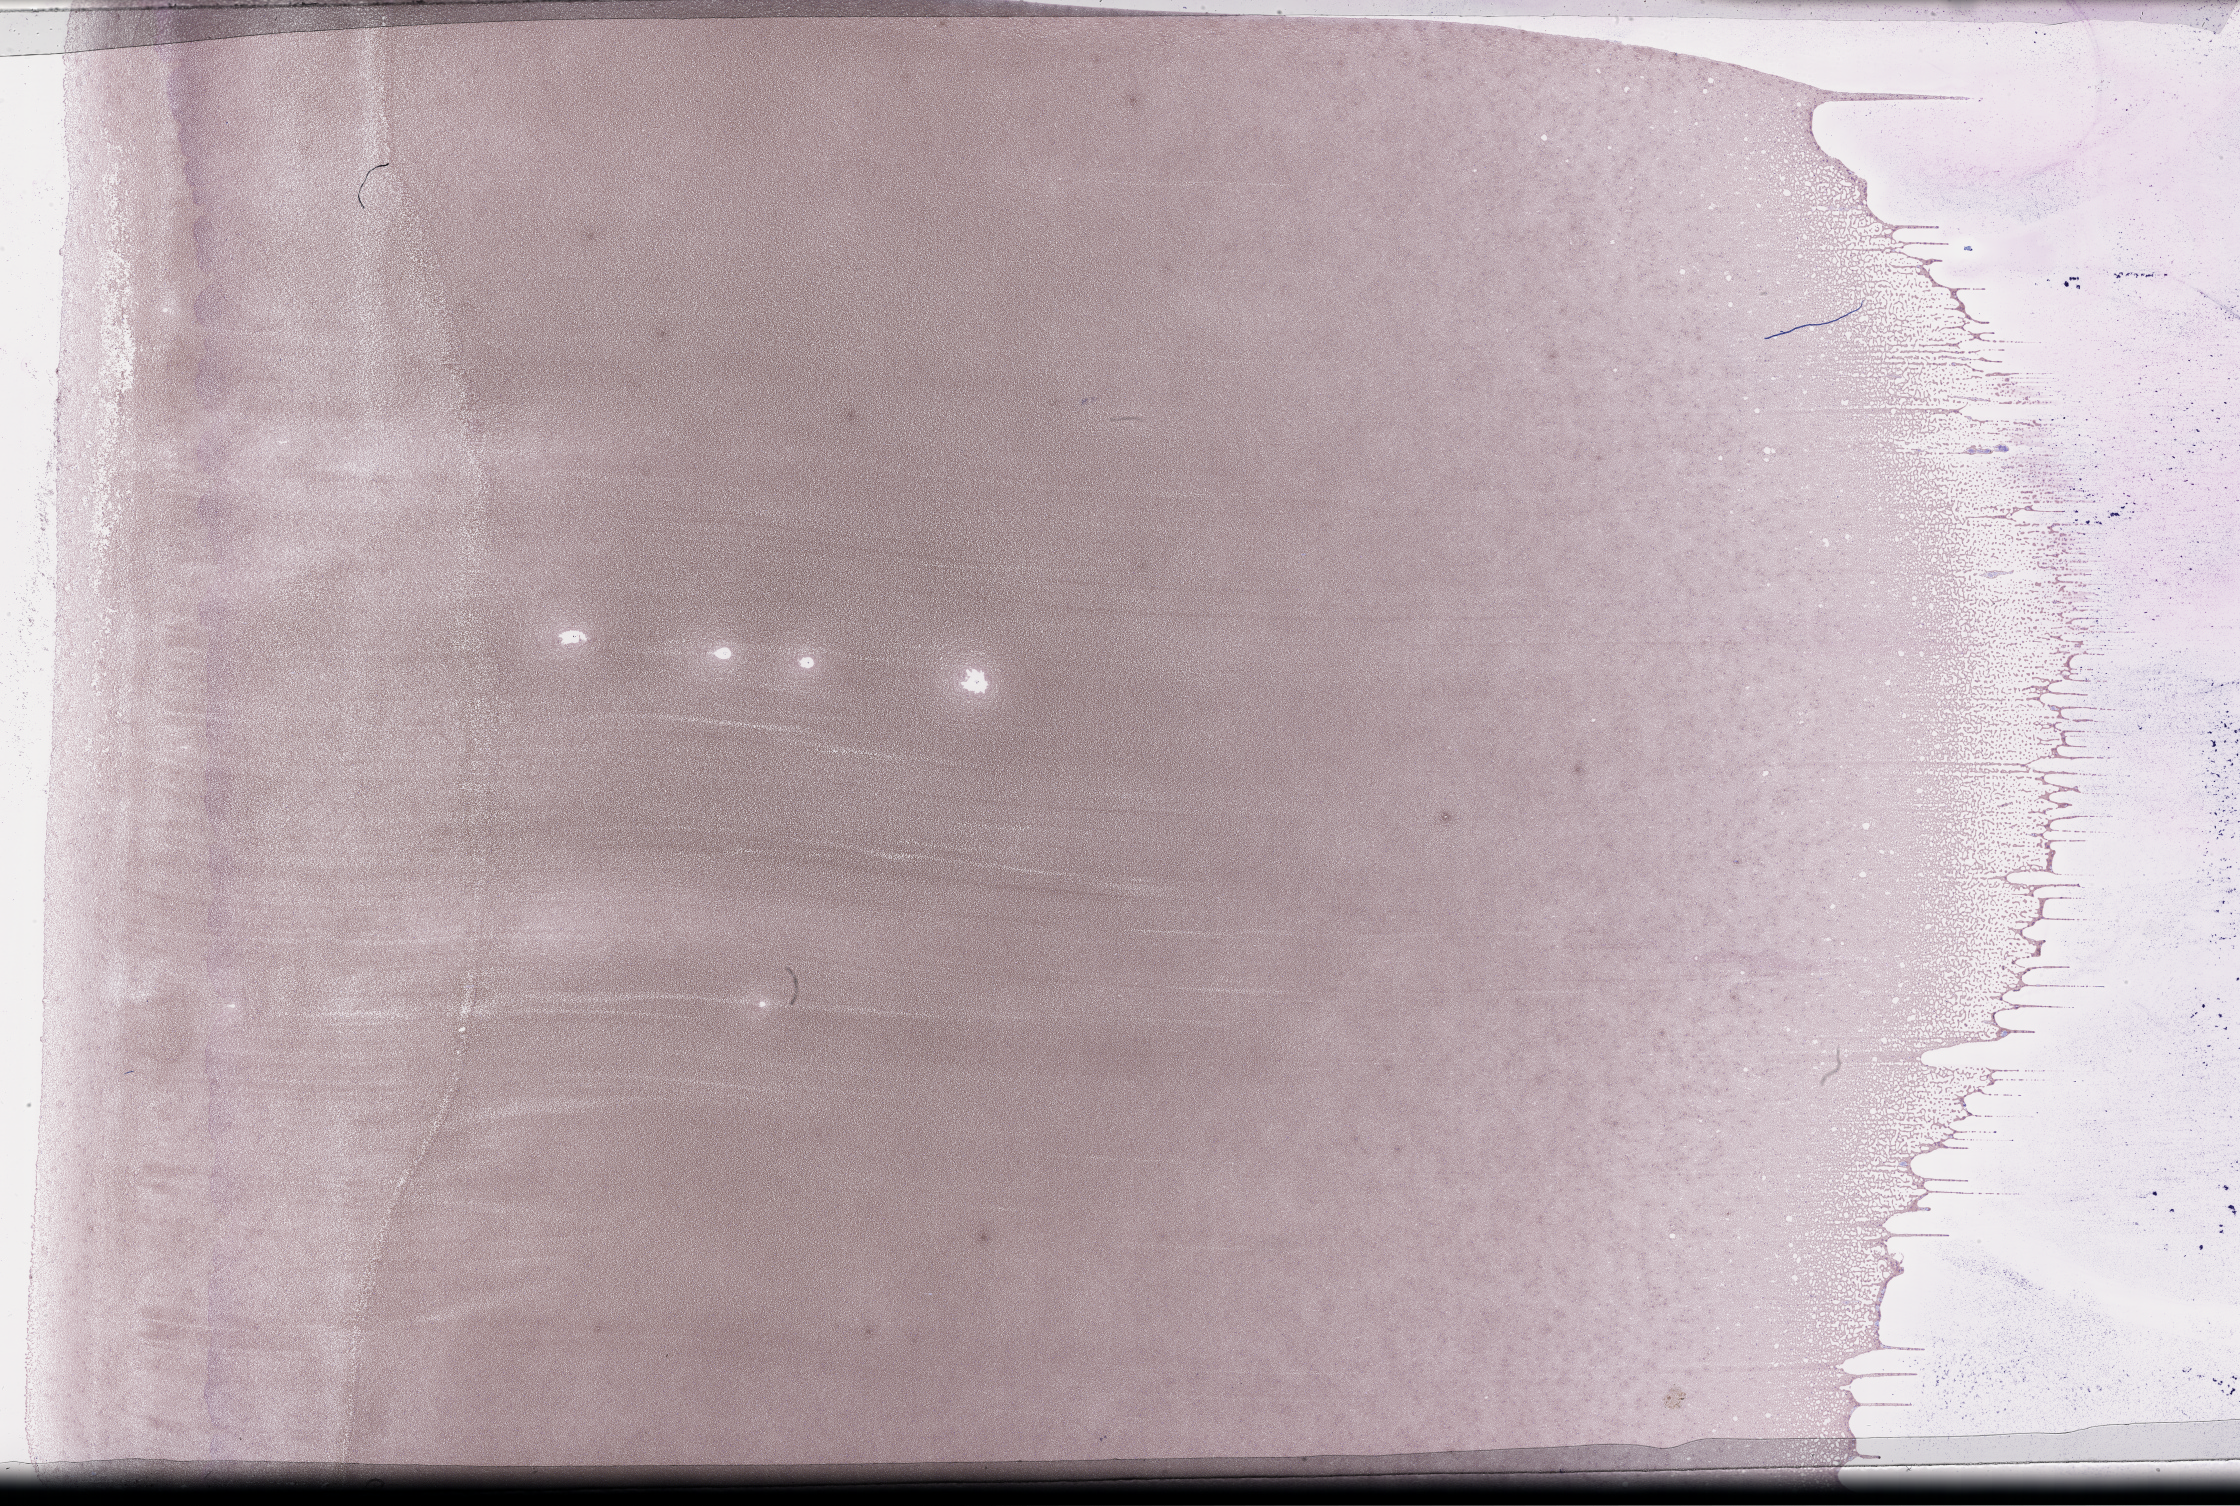
Whole-slide image of a whole blood smear, Wright-Giemsa stain, a low-resolution overview of the entire scanned area, about 36.2 x 24.3 mm; collected on treatment. Patient sex: female.
Patient diagnosis: Plasma Cell Myeloma.